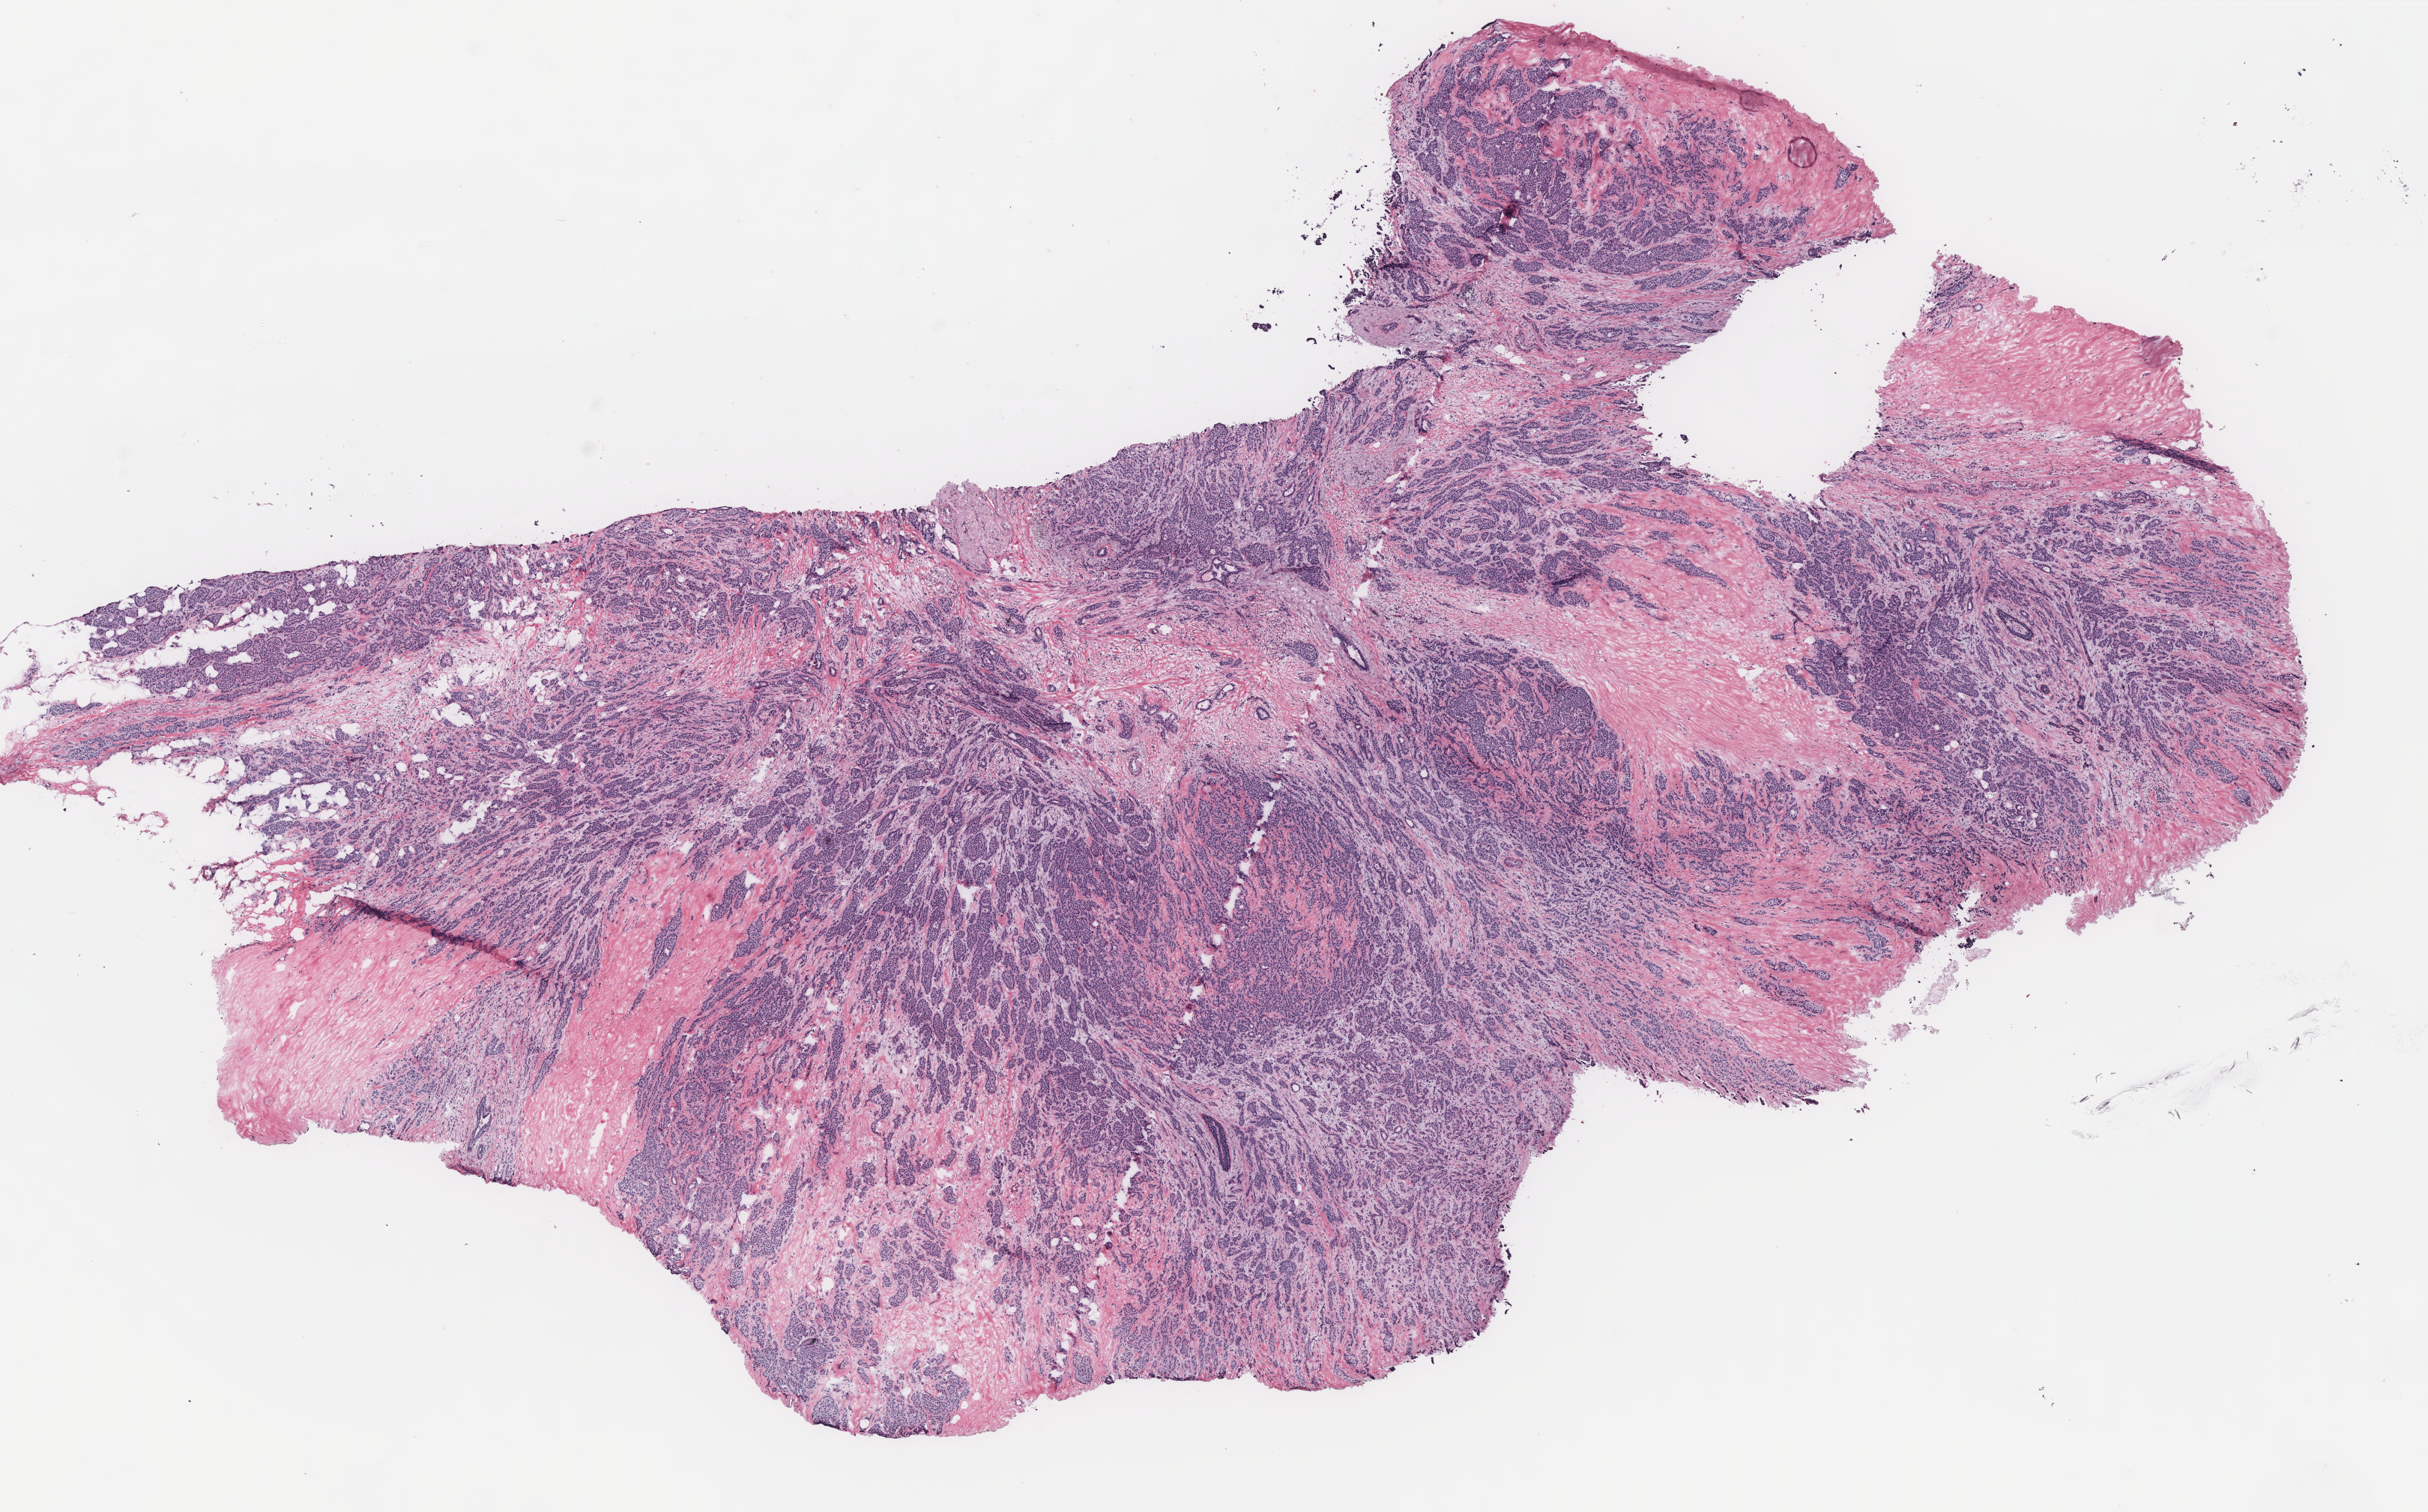
H&E whole-slide image — shown as a low-resolution overview of the whole scanned area (about 13.0 x 8.1 mm, acquisition: 40x scan); breast, tumour tissue. Patient: female, age 51 years.
* diagnosis: Infiltrating duct carcinoma, NOS
* AJCC pathologic stage: IIB